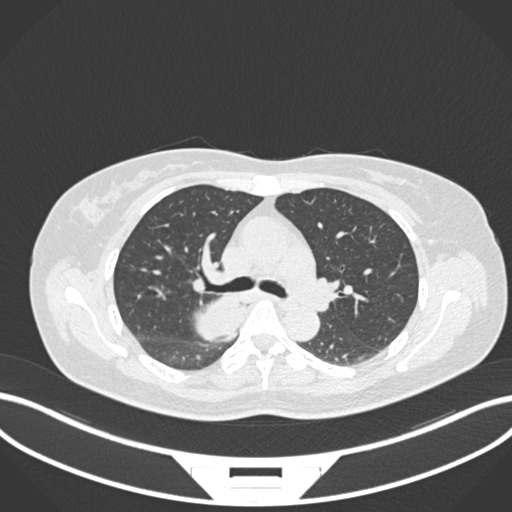
Chest CT, one axial slice. Slice 620 of 677 in the series (ordered by position). Reconstruction kernel B30f. 120 kVp. Lung window (W 1500 / L -600 HU). 1 mm slice thickness. 512 × 512 image matrix, field of view 400 × 400 mm. Female patient, age 54 years. From the clinical record (not read from this slice): clinical TNM (as recorded): T4 N0 M0.
Structures marked on this image (rectangle marked by the reading radiologist):
- lung tumour (recorded histology: adenocarcinoma): bounding box [x1, y1, x2, y2] px = [187, 286, 247, 343]